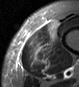
MRI of an extremity soft-tissue mass, one axial slice. Position 8 of 45 along the scan axis. STIR. MR volume resampled by the dataset authors to the PET/CT grid (not the native acquisition matrix). 3.27 mm slice thickness. 79 × 87 image matrix, field of view 77 × 85 mm. Male patient. From the clinical record (not read from this slice): histological type: pleiomorphic leiomyosarcoma; grade: high; site of the primary tumour: left thigh.
Annotated regions visible in this slice (expert contour drawn on MRI and transferred to this co-registered scan by the dataset authors):
- gross tumour volume including surrounding oedema: bounding box [x1, y1, x2, y2] px = [34, 23, 57, 53]